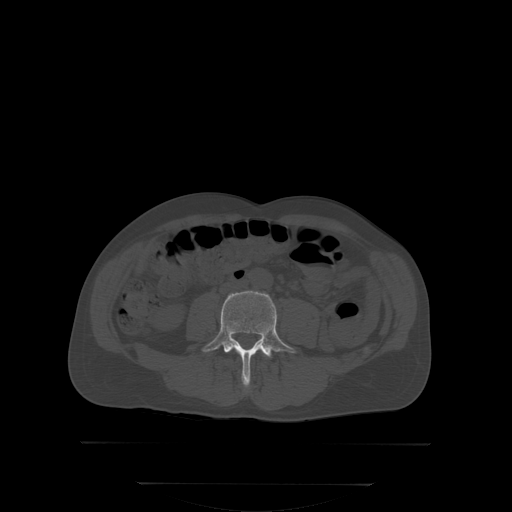
CT including the spine, one axial slice; position 110 of 350 along the scan axis; bone window (W 1800 / L 400 HU); 512 × 512 image matrix, field of view 500 × 500 mm. Male patient, age 58 years. From the clinical record (not read from this slice): primary cancer: prostate; vertebrae with lytic lesions (as recorded): L1.
Outlined on this slice (semi-automatic segmentation, software-assisted and operator-edited):
- L4 vertebra: box from (x=202, y=290) to (x=296, y=388) px